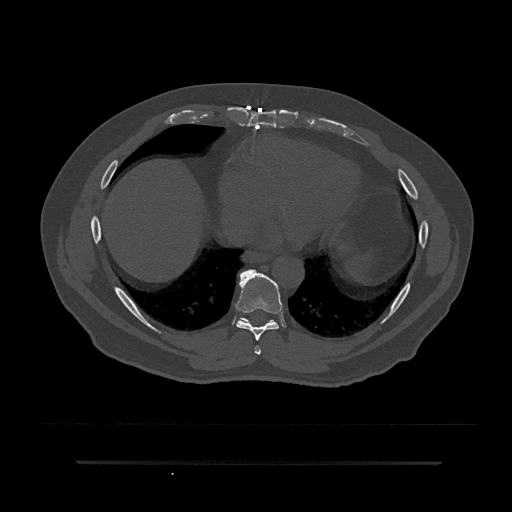
CT including the spine, one axial slice; reconstruction kernel Br40s/3; 120 kVp; bone window (W 1800 / L 400 HU); 0.5 mm slice thickness; 512 × 512 image matrix, field of view 464 × 464 mm. Male patient, age 59 years. From the clinical record (not read from this slice): primary cancer: bile ducts.
Structures marked on this image (semi-automatic segmentation, software-assisted and operator-edited):
- T7 vertebra: bounding box [x1, y1, x2, y2] px = [254, 346, 261, 355]
- T8 vertebra: [236, 269, 283, 341]
- T9 vertebra: [240, 318, 274, 321]